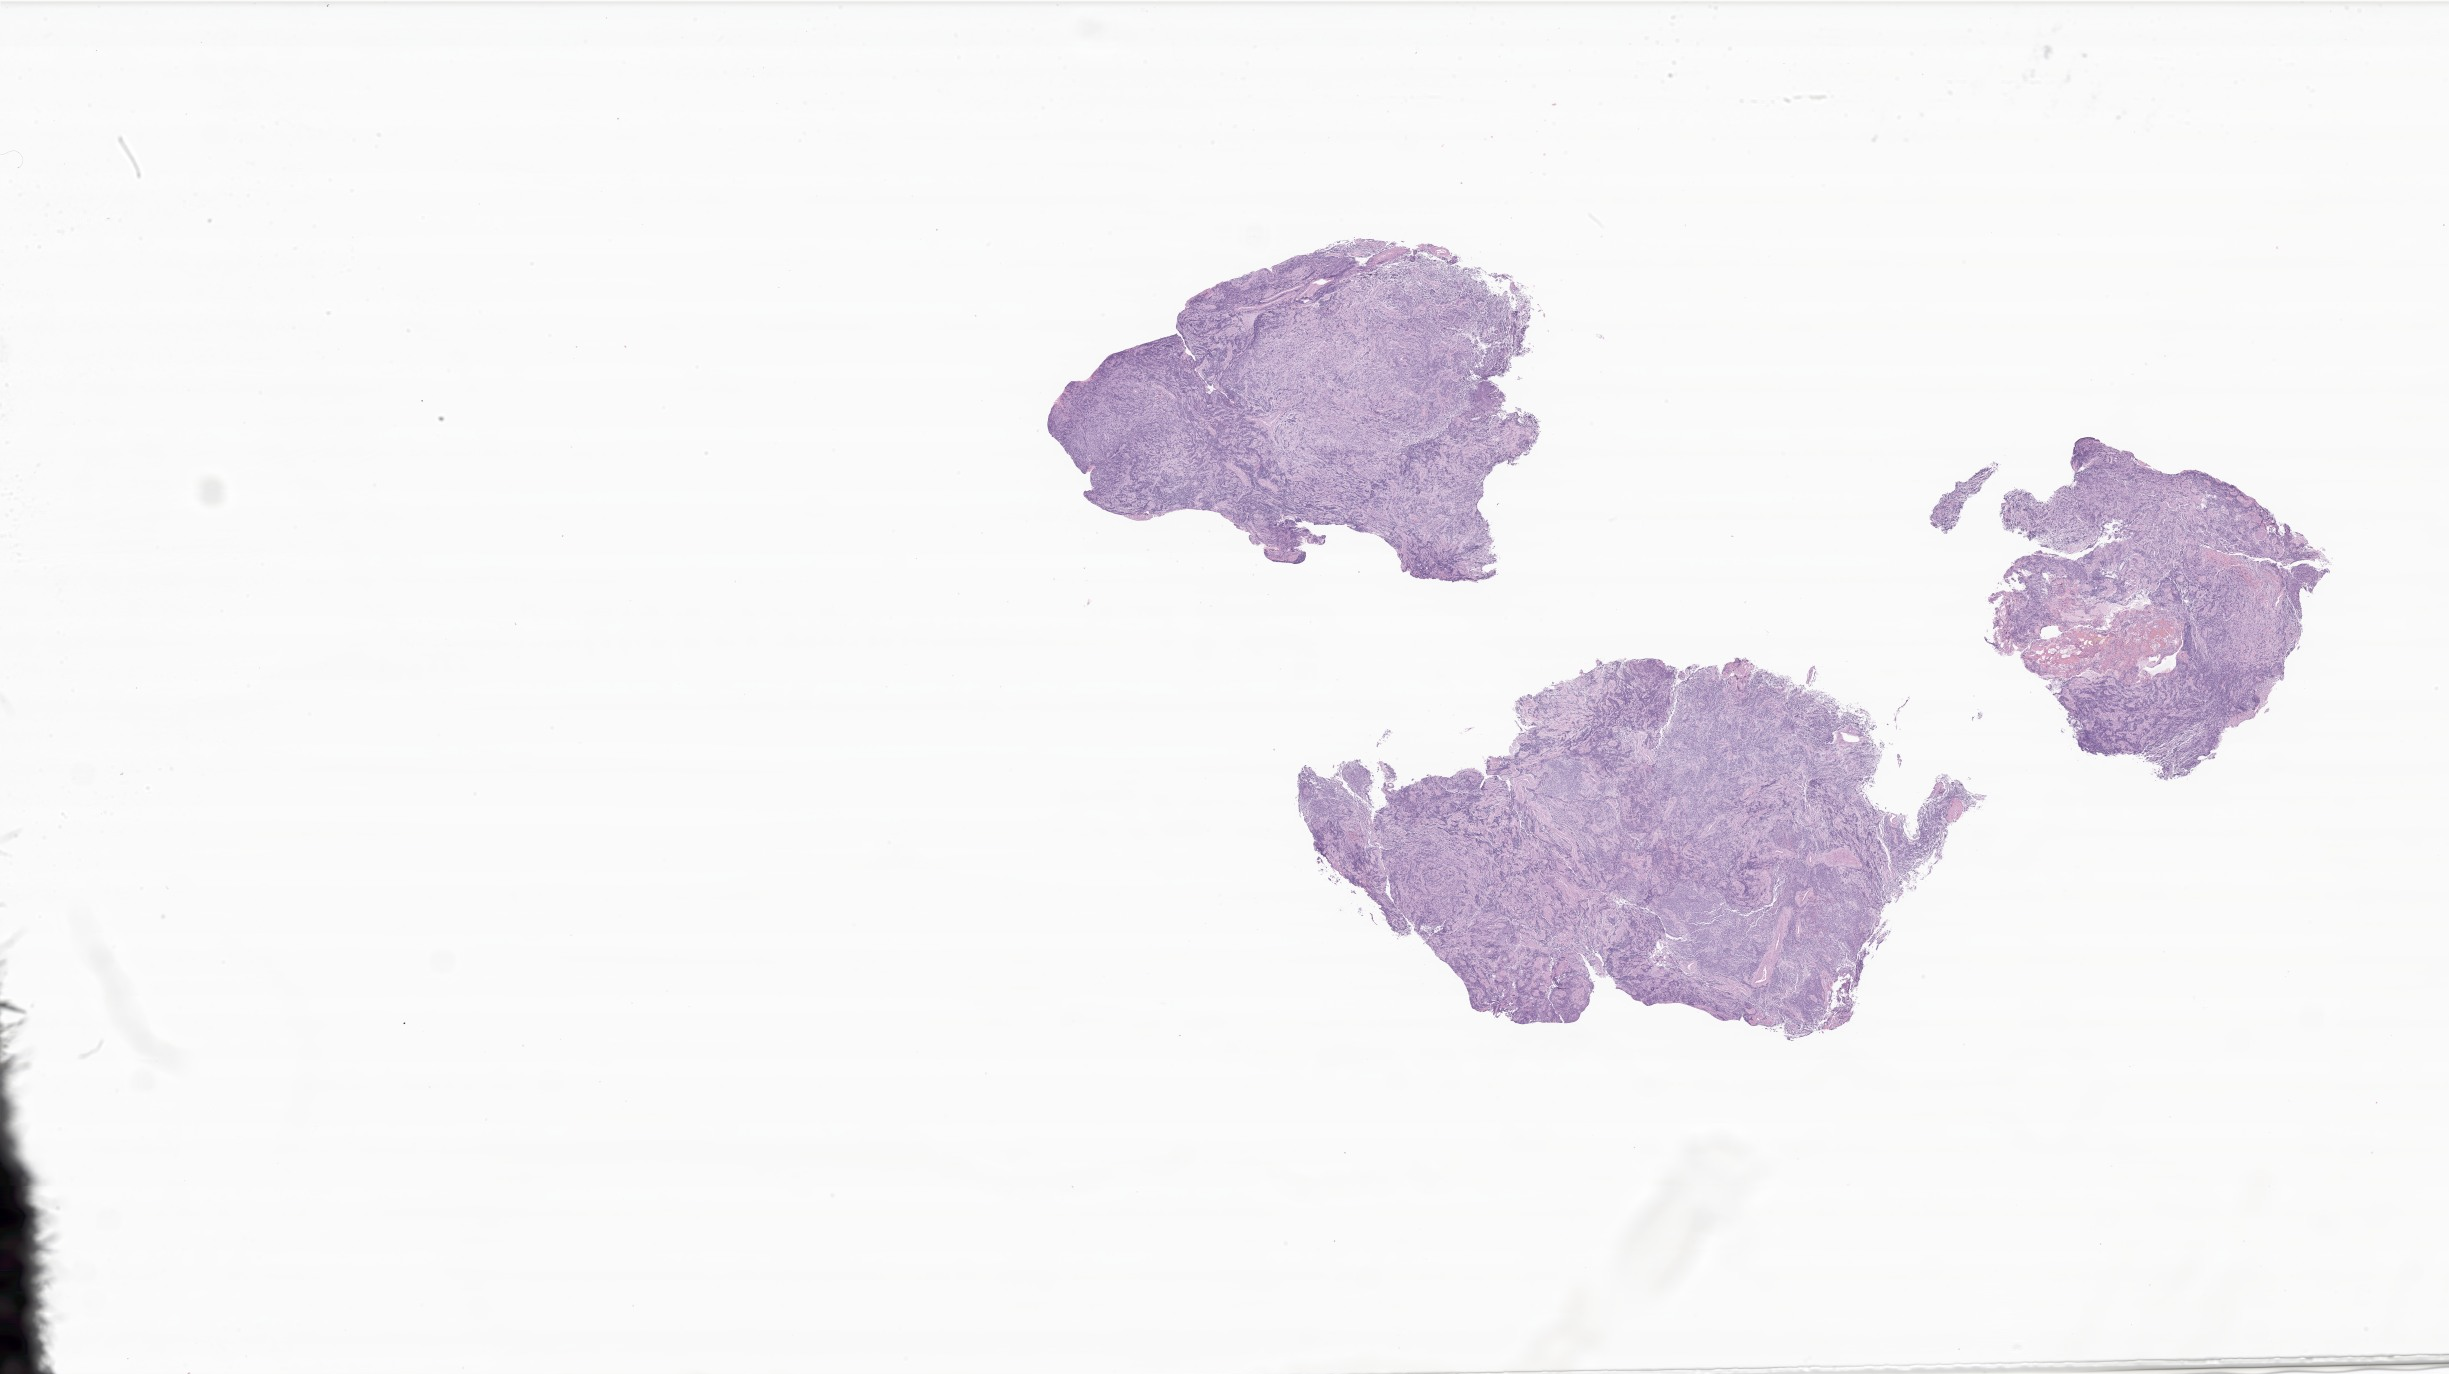
Whole-slide image, haematoxylin and eosin stain of tumor tissue from the brain, whole scanned area (about 41.3 x 23.2 mm) shown as a low-resolution overview; formalin-fixed paraffin-embedded section. Patient male; age 72 months (6 years).
Diagnosis: Medulloblastoma, NOS.